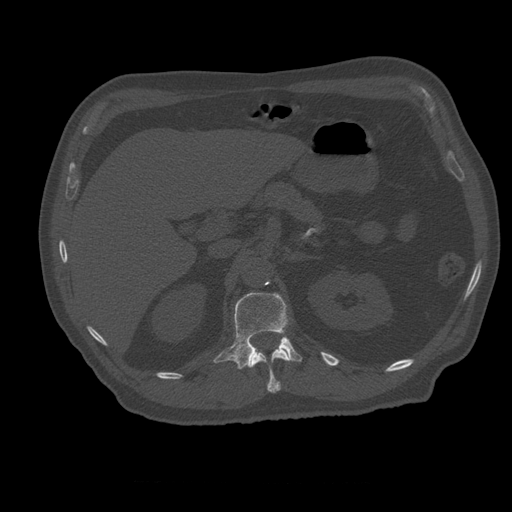
CT including the spine, one axial slice. Position 246 of 399 along the scan axis. Reconstruction kernel STANDARD. 120 kVp. Bone window (W 1800 / L 400 HU). 1.25 mm slice thickness. 512 × 512 image matrix, field of view 407 × 407 mm. Patient age 73 years. From the clinical record (not read from this slice): primary cancer: prostate.
Outlined on this slice (semi-automatically segmented with operator editing):
- L1 vertebra: bounding box [x1, y1, x2, y2] px = [214, 293, 302, 370]
- T12 vertebra: [249, 348, 291, 393]